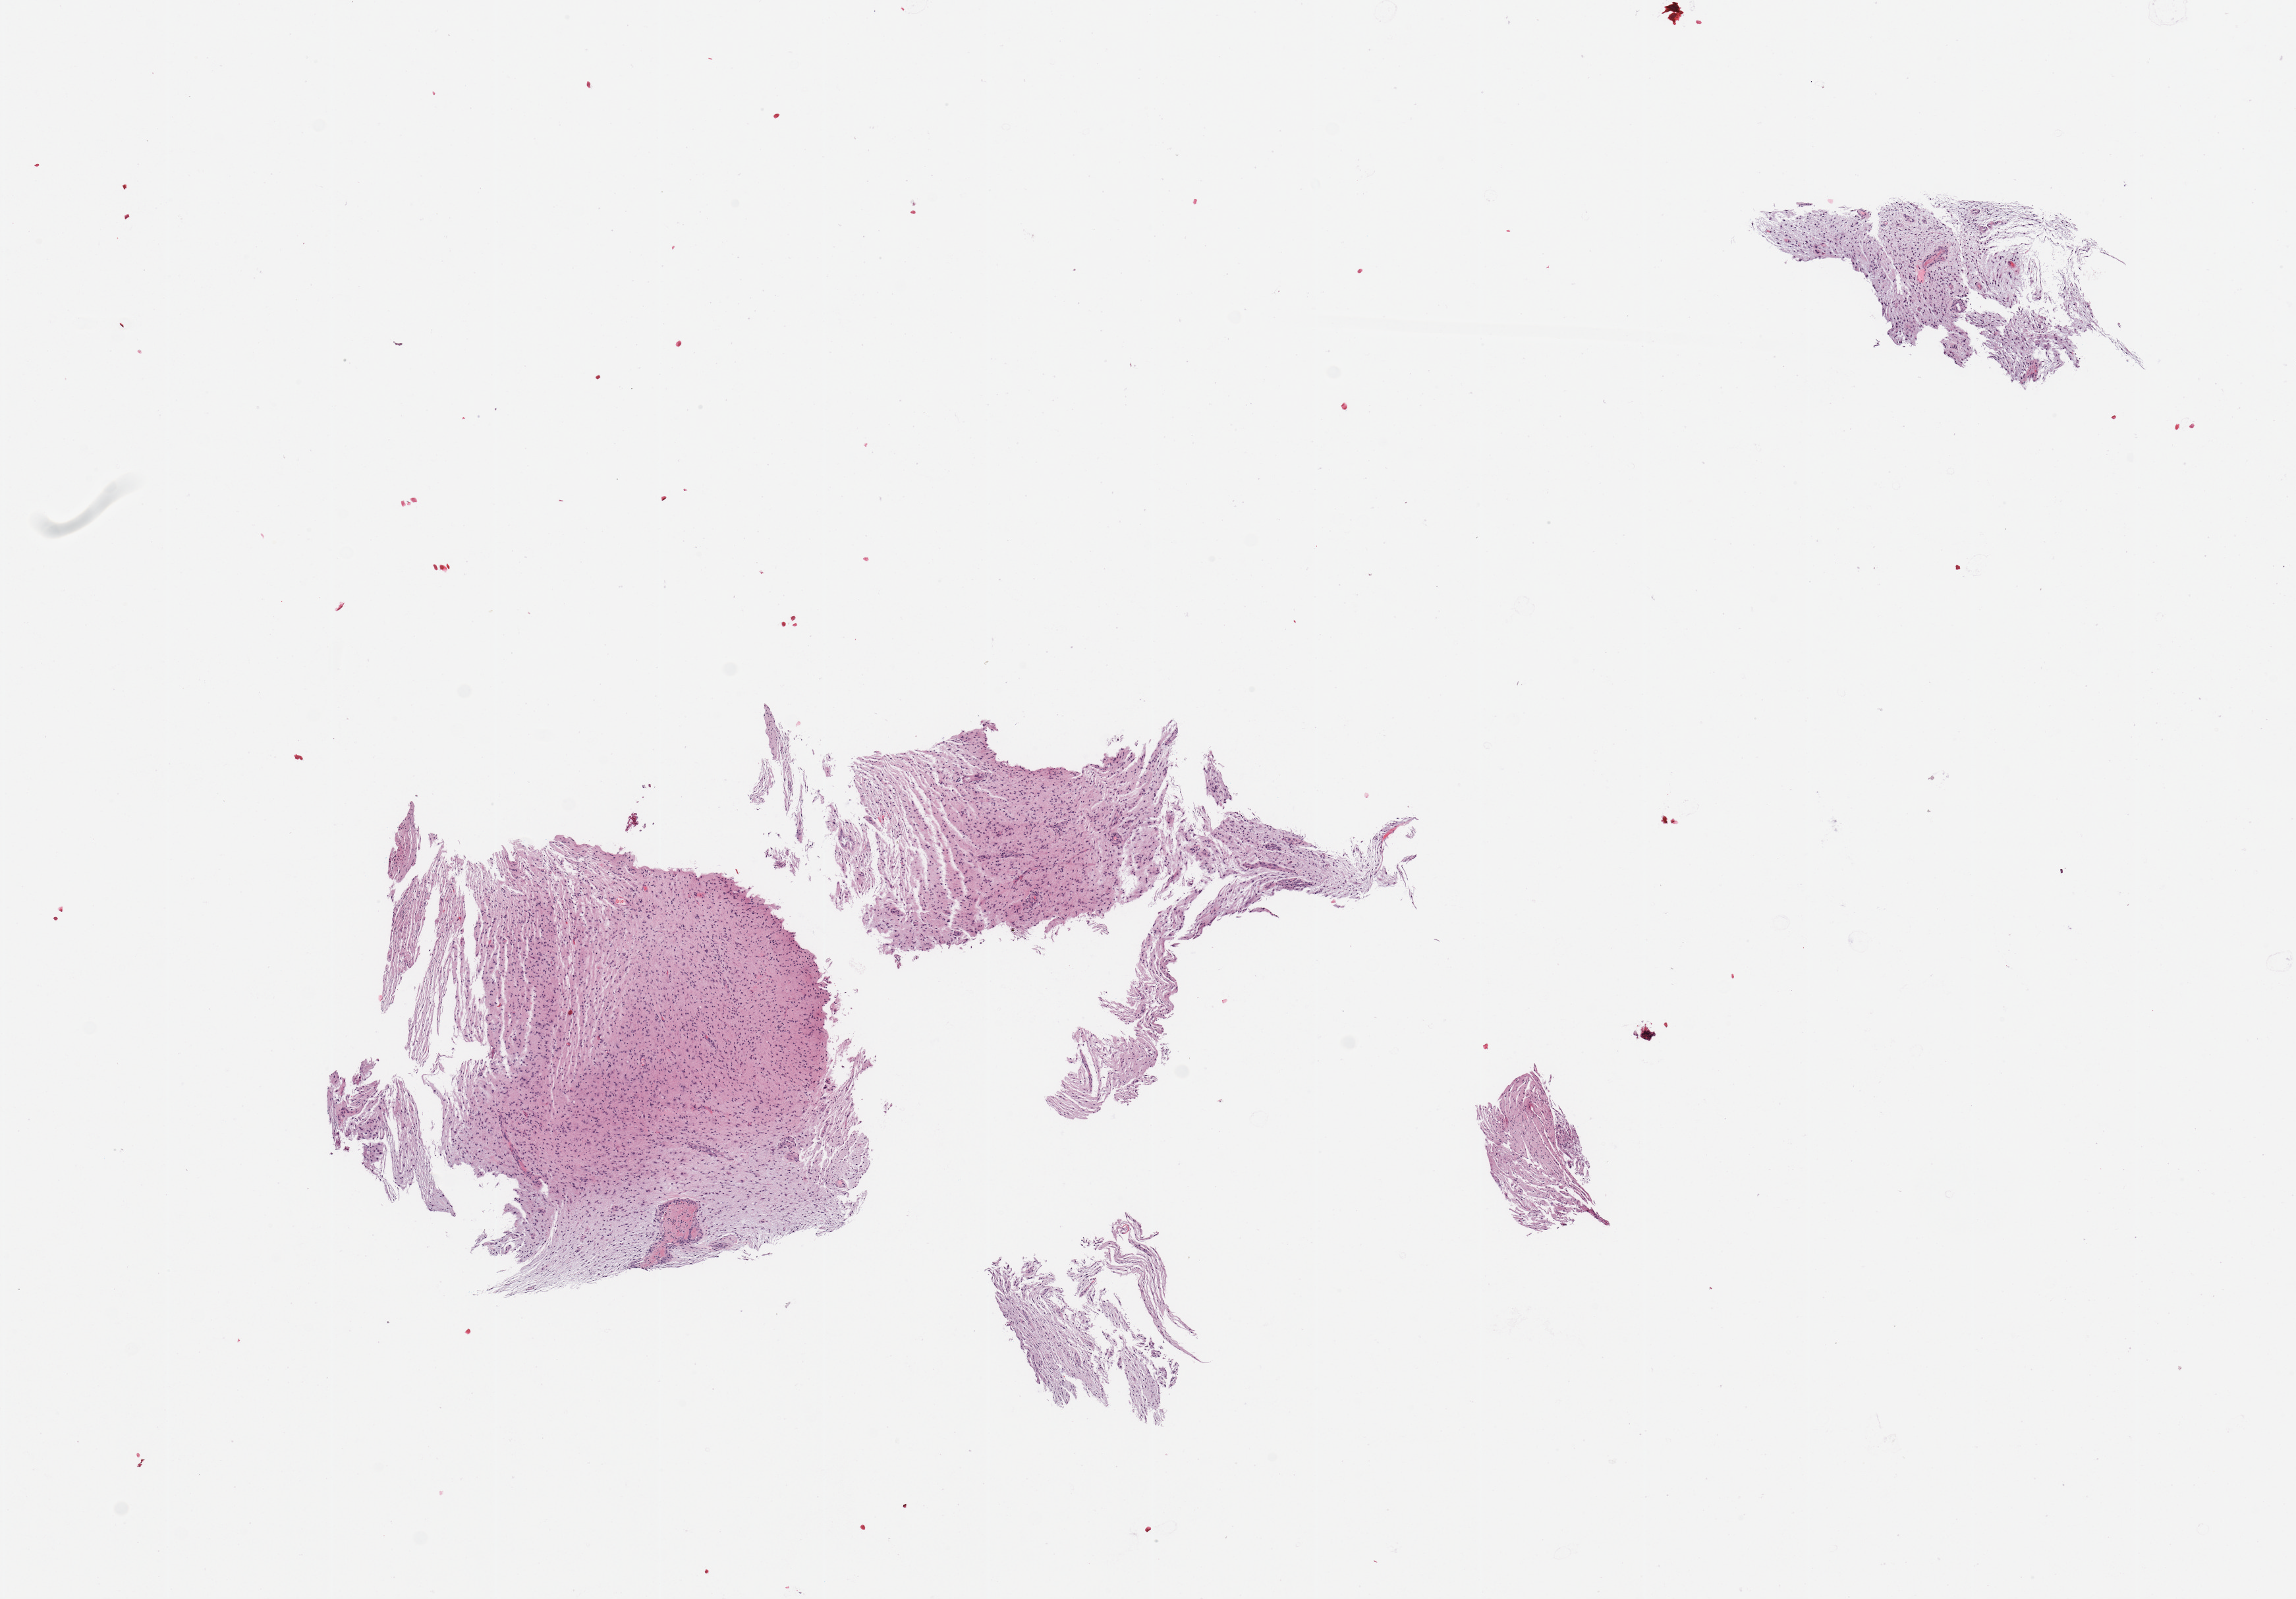
Digitized H&E tissue section (whole slide), shown as a low-resolution overview of the whole scanned area (about 13.8 x 9.6 mm, from a 20x scan); tumour tissue sample, sampled site: frontal lobe. Patient: female, age 57 years. Slide review estimates, as recorded: tumour nuclei 70%, necrosis 5%.
Diagnosis: Glioblastoma.